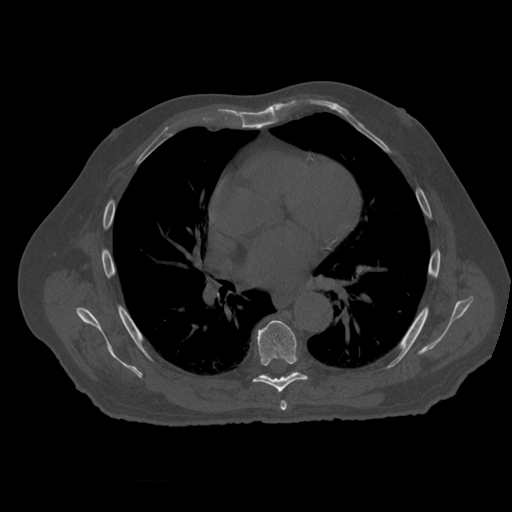
CT including the spine, one axial slice; position 361 of 399 along the scan axis; reconstruction kernel STANDARD; bone window (W 1800 / L 400 HU); 512 × 512 image matrix. Patient age 73 years. Case-level facts recorded for this patient, not image findings: primary cancer: prostate.
Annotated regions visible in this slice (semi-automatic segmentation, software-assisted and operator-edited):
- T6 vertebra: bounding box [x1, y1, x2, y2] px = [281, 401, 287, 412]
- T7 vertebra: [254, 321, 308, 393]